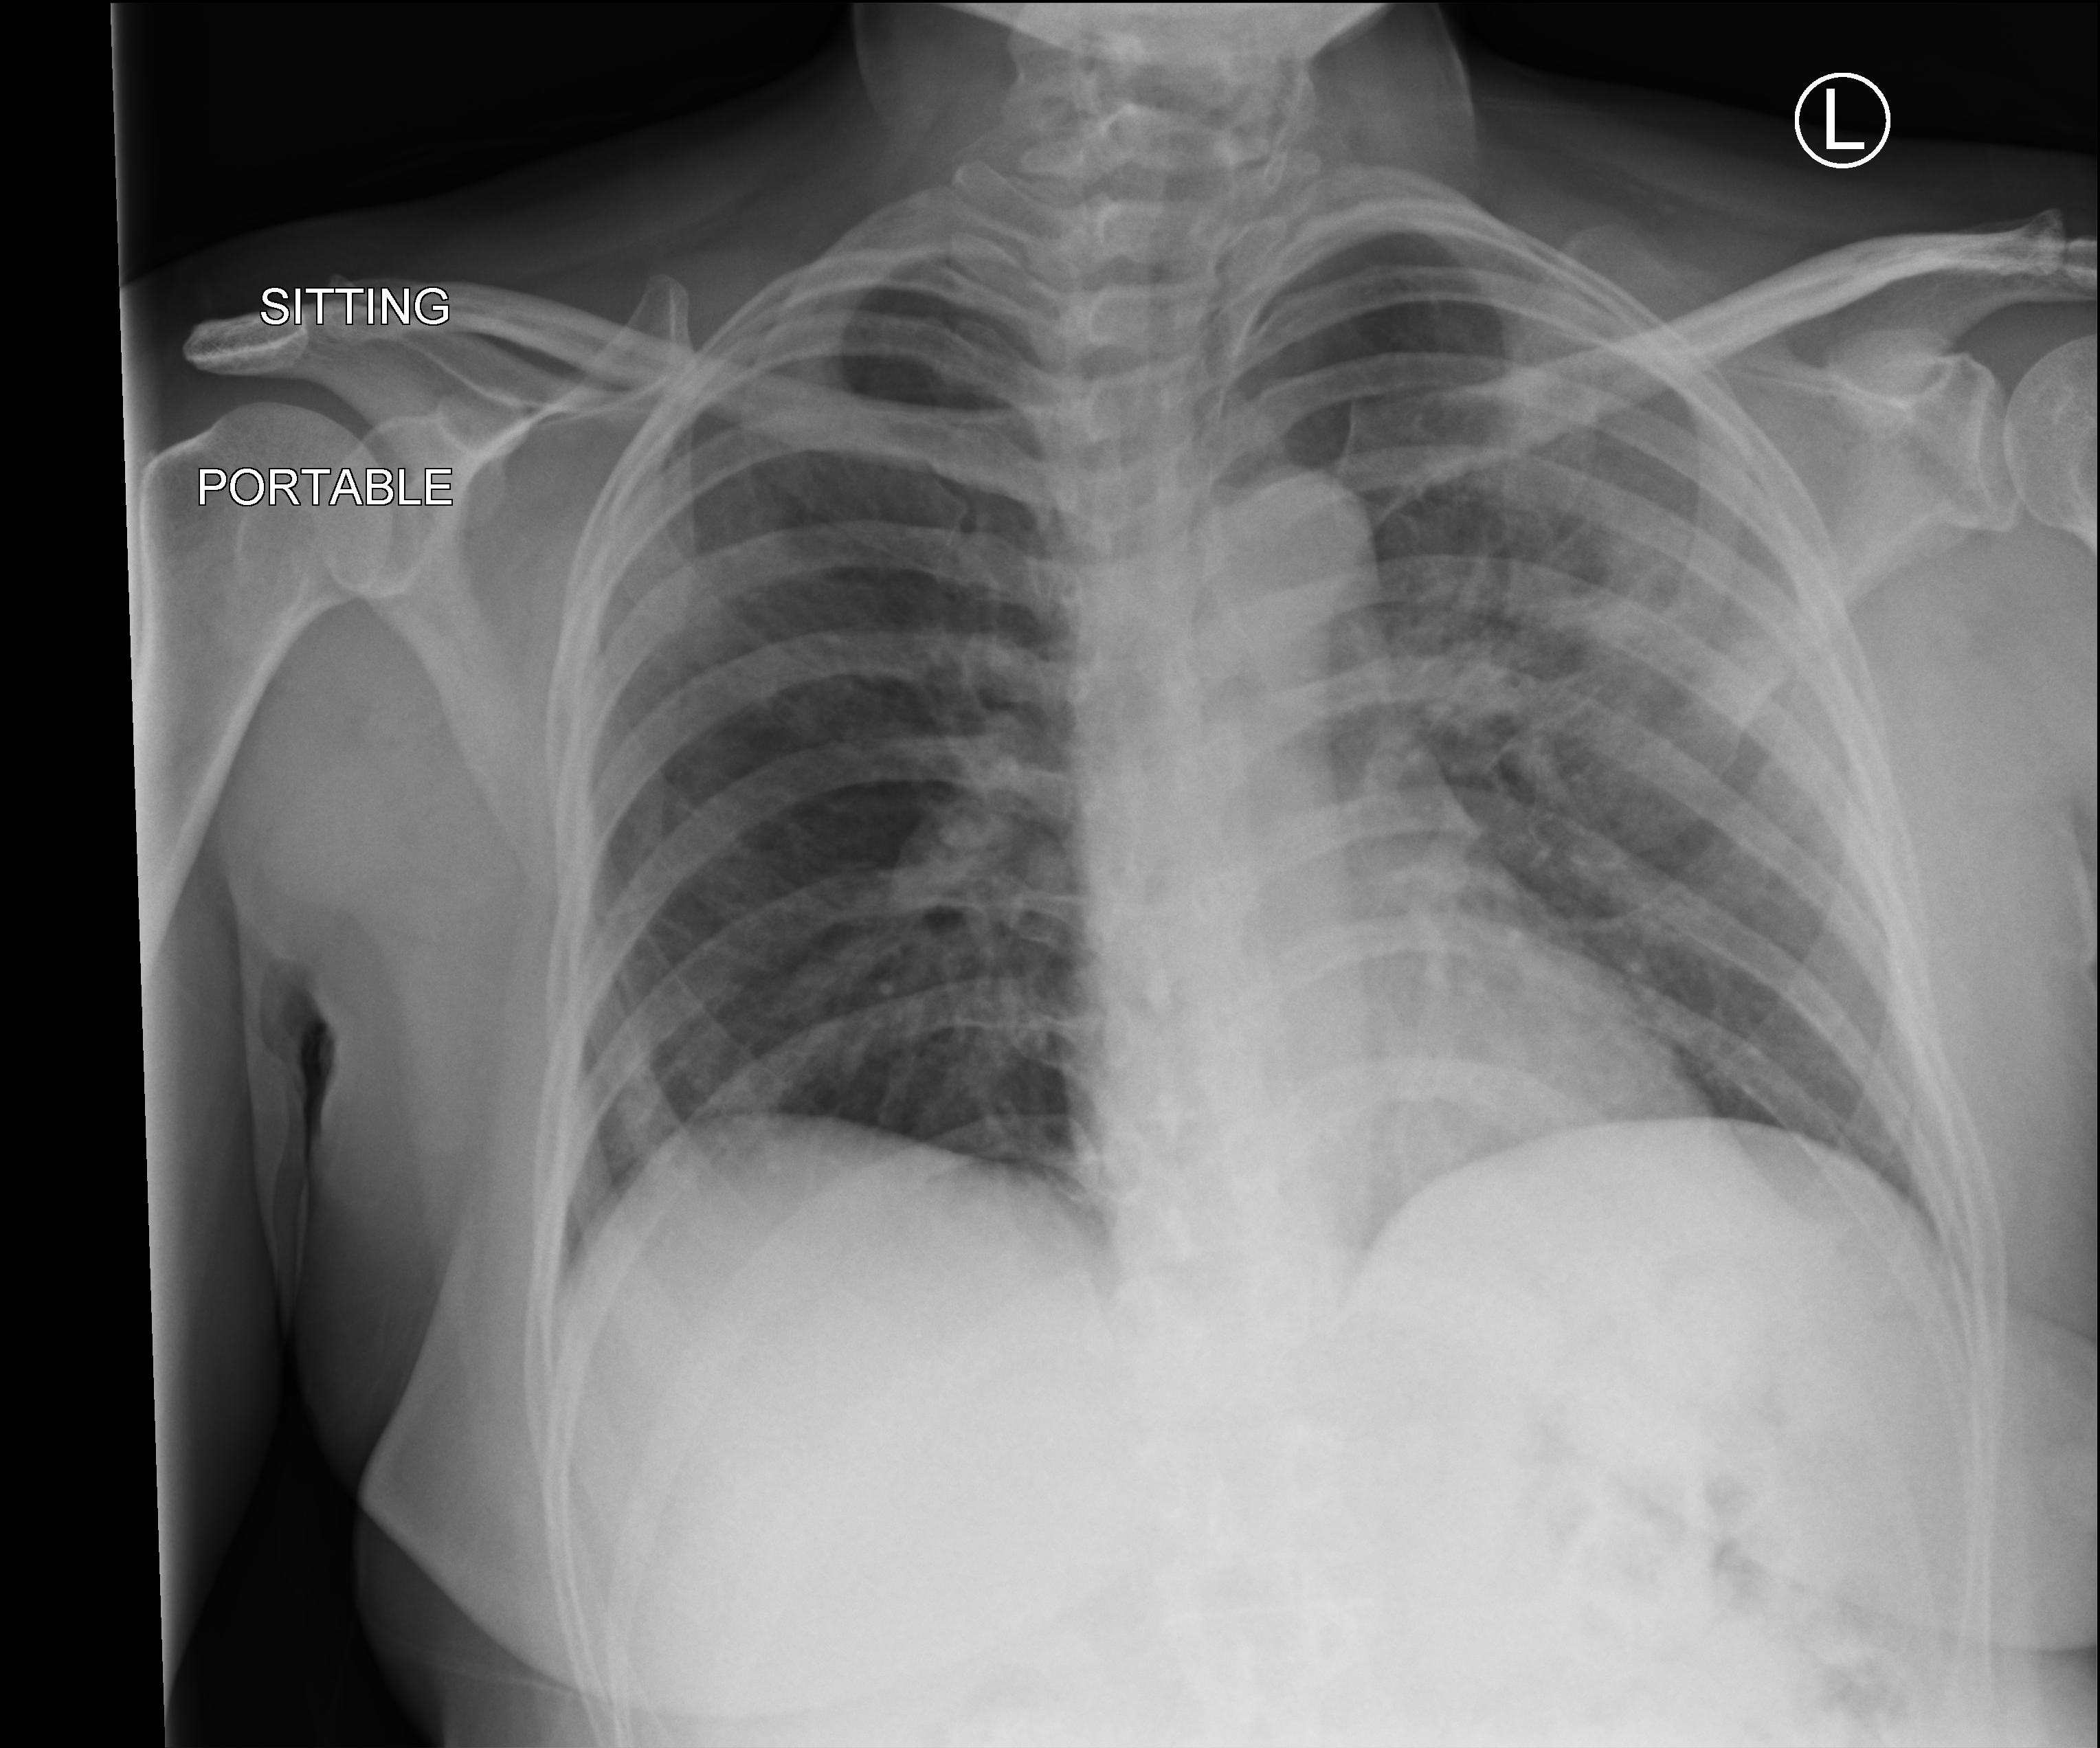
Chest X-ray (portable); anteroposterior (AP) projection. Patient hospitalised with COVID-19; female, aged 18–59 years.
Hospital-stay facts (about this admission, not read from this image; timing relative to this image not recorded):
- admitted to intensive care during this hospital stay: yes
- mechanically ventilated during this hospital stay: no